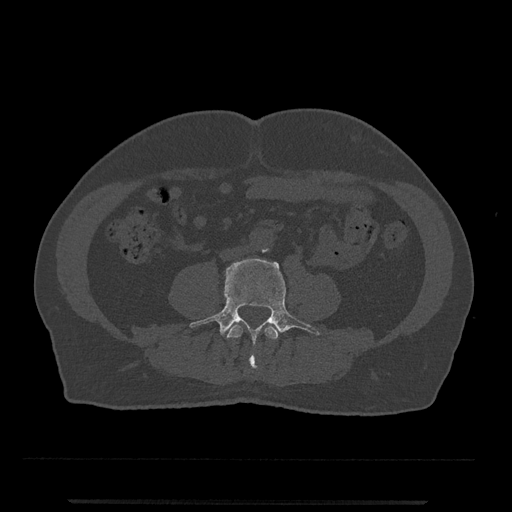
CT including the spine, one axial slice; slice 152 of 797 in the series (ordered by position); bone window (W 1800 / L 400 HU); 0.5 mm slice thickness; 512 × 512 image matrix, field of view 419 × 419 mm. Male patient, age 63 years. Case-level facts recorded for this patient, not image findings: primary cancer: prostate.
Annotated regions visible in this slice (semi-automatic segmentation, software-assisted and operator-edited):
- L3 vertebra: bounding box [x1, y1, x2, y2] px = [226, 324, 279, 369]
- L4 vertebra: [189, 258, 320, 365]